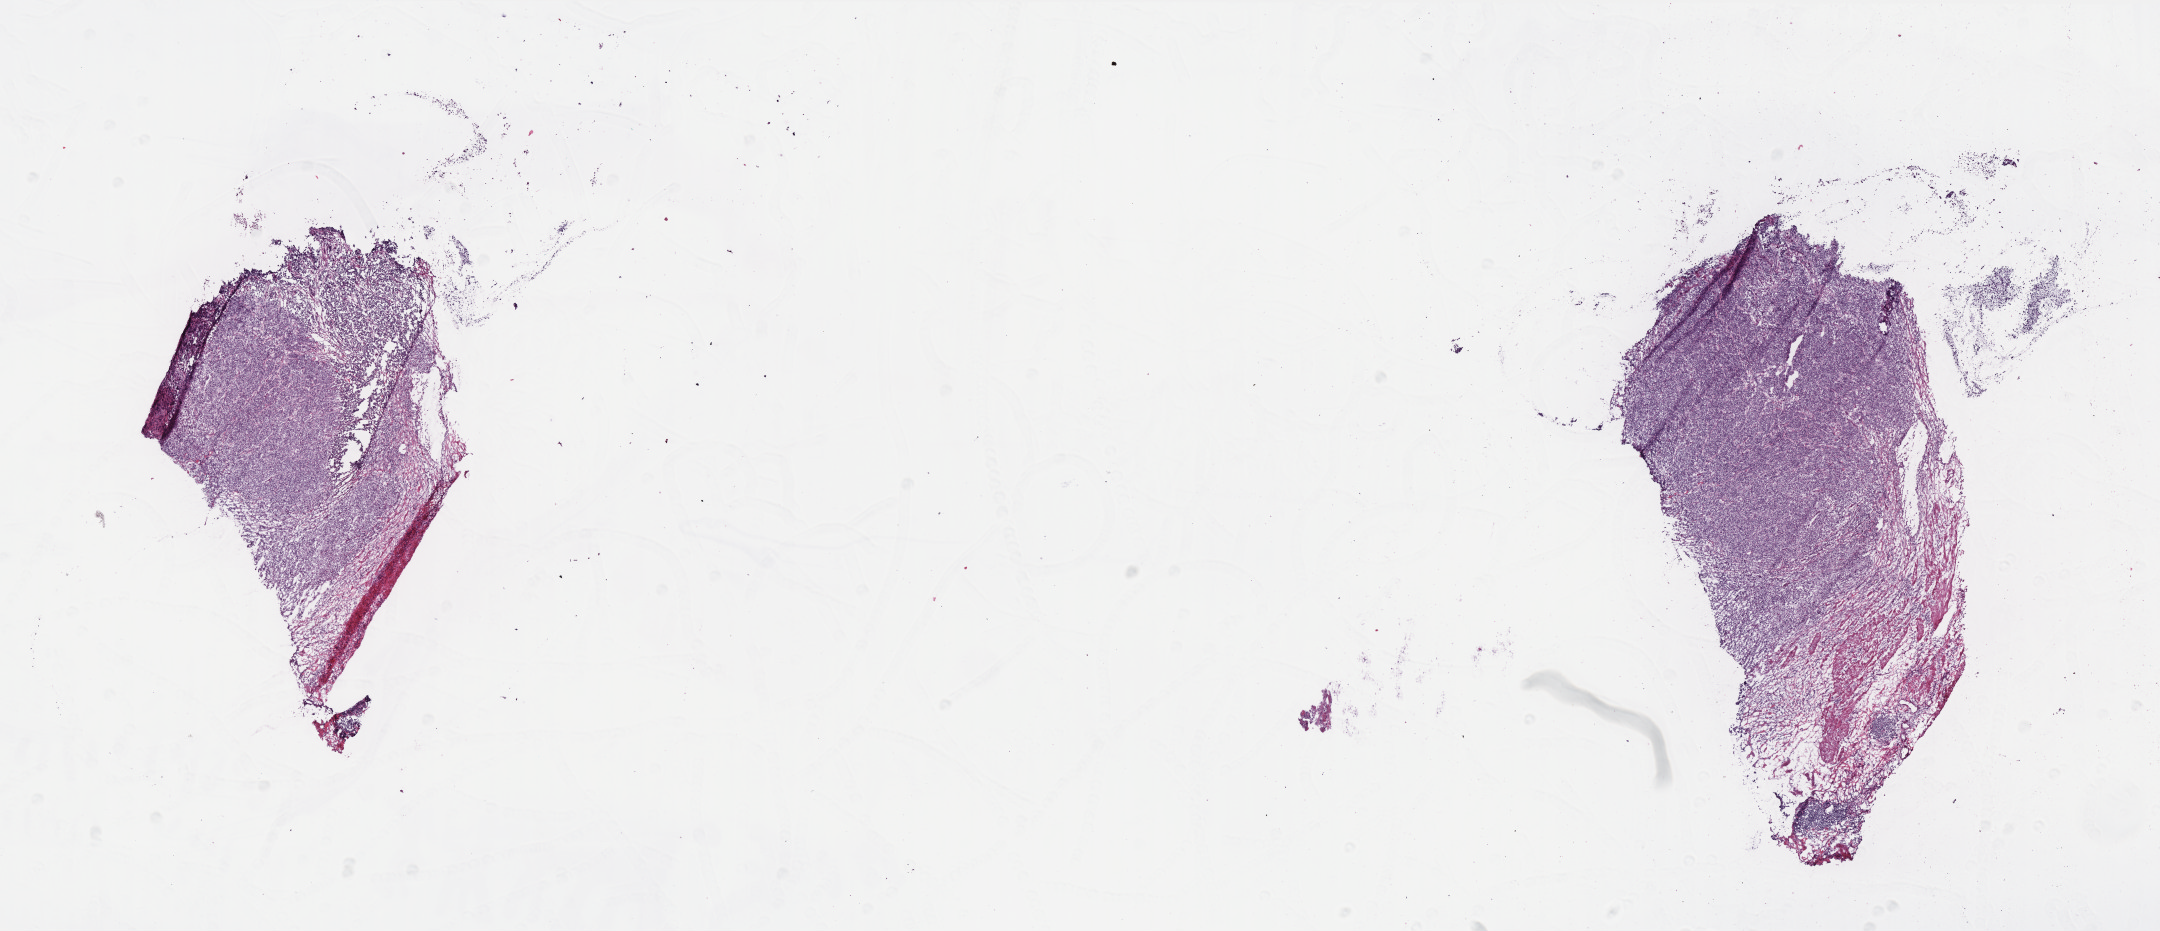
H&E-stained whole-slide image — whole scanned area (about 17.3 x 7.5 mm, slide scanned at 40x) shown as a low-resolution overview; frozen section from the bottom of the tissue portion; primary tumour sample from the colon. Female, age 64 years at initial diagnosis.
Diagnosis: Adenocarcinoma, NOS (cecum).